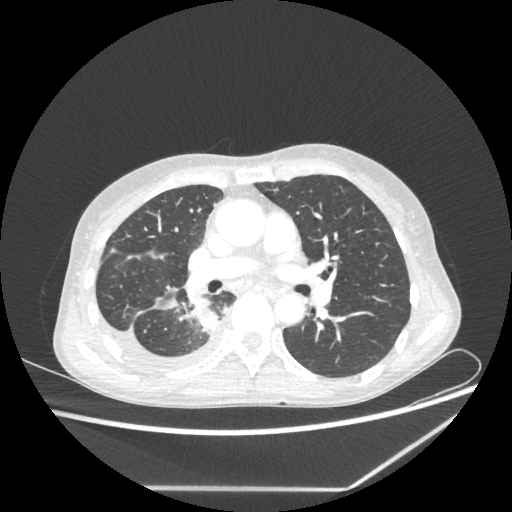
Chest CT, one axial slice; slice 129 of 237 in the series (ordered by position); reconstruction kernel STANDARD; lung window (W 1500 / L -600 HU); 1.25 mm slice thickness; 512 × 512 image matrix, field of view 364 × 364 mm. Female patient, age 59 years. From the clinical record (not read from this slice): clinical TNM (as recorded): T1c N1 M1.
Structures marked on this image (bounding box drawn by a radiologist):
- lung tumour (recorded histology: adenocarcinoma): bounding box <193,302,224,337> (left, top, right, bottom; pixels)